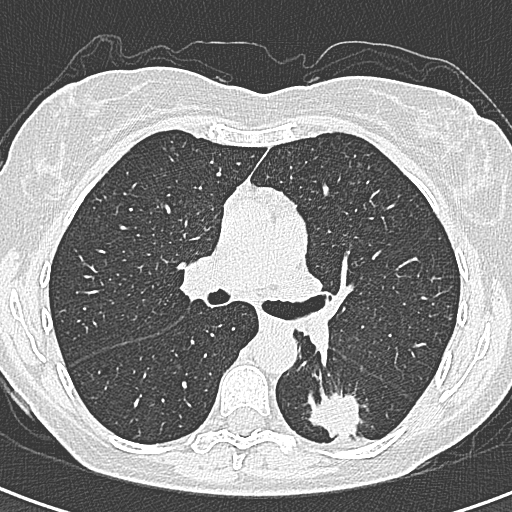
Axial slice from a low-dose chest CT screening exam; baseline screening round; lung window (W 1500 / L -600 HU); 1 mm slice thickness; lung (sharp) reconstruction kernel (B80f); 120 kVp. Female participant, aged 58 years at enrolment. Former smoker at enrolment.
Lesion marked by an expert reader, bounding box <294,389,364,456> (left, top, right, bottom; pixels). The screening reader recorded 2 non-calcified nodules or masses ≥4 mm on this exam (left lower lobe, right lower lobe); which of them this box marks is not recorded. Official screen result: positive, change unspecified: nodule(s) >= 4 mm or enlarging nodule(s), mass(es), or other non-specific abnormalities suspicious for lung cancer. Later outcome: lung cancer diagnosed 22 days after this screen — adenocarcinoma, NOS, left lower lobe, moderately differentiated (G2), stage IA (AJCC 6th edition), 25 mm at pathology.